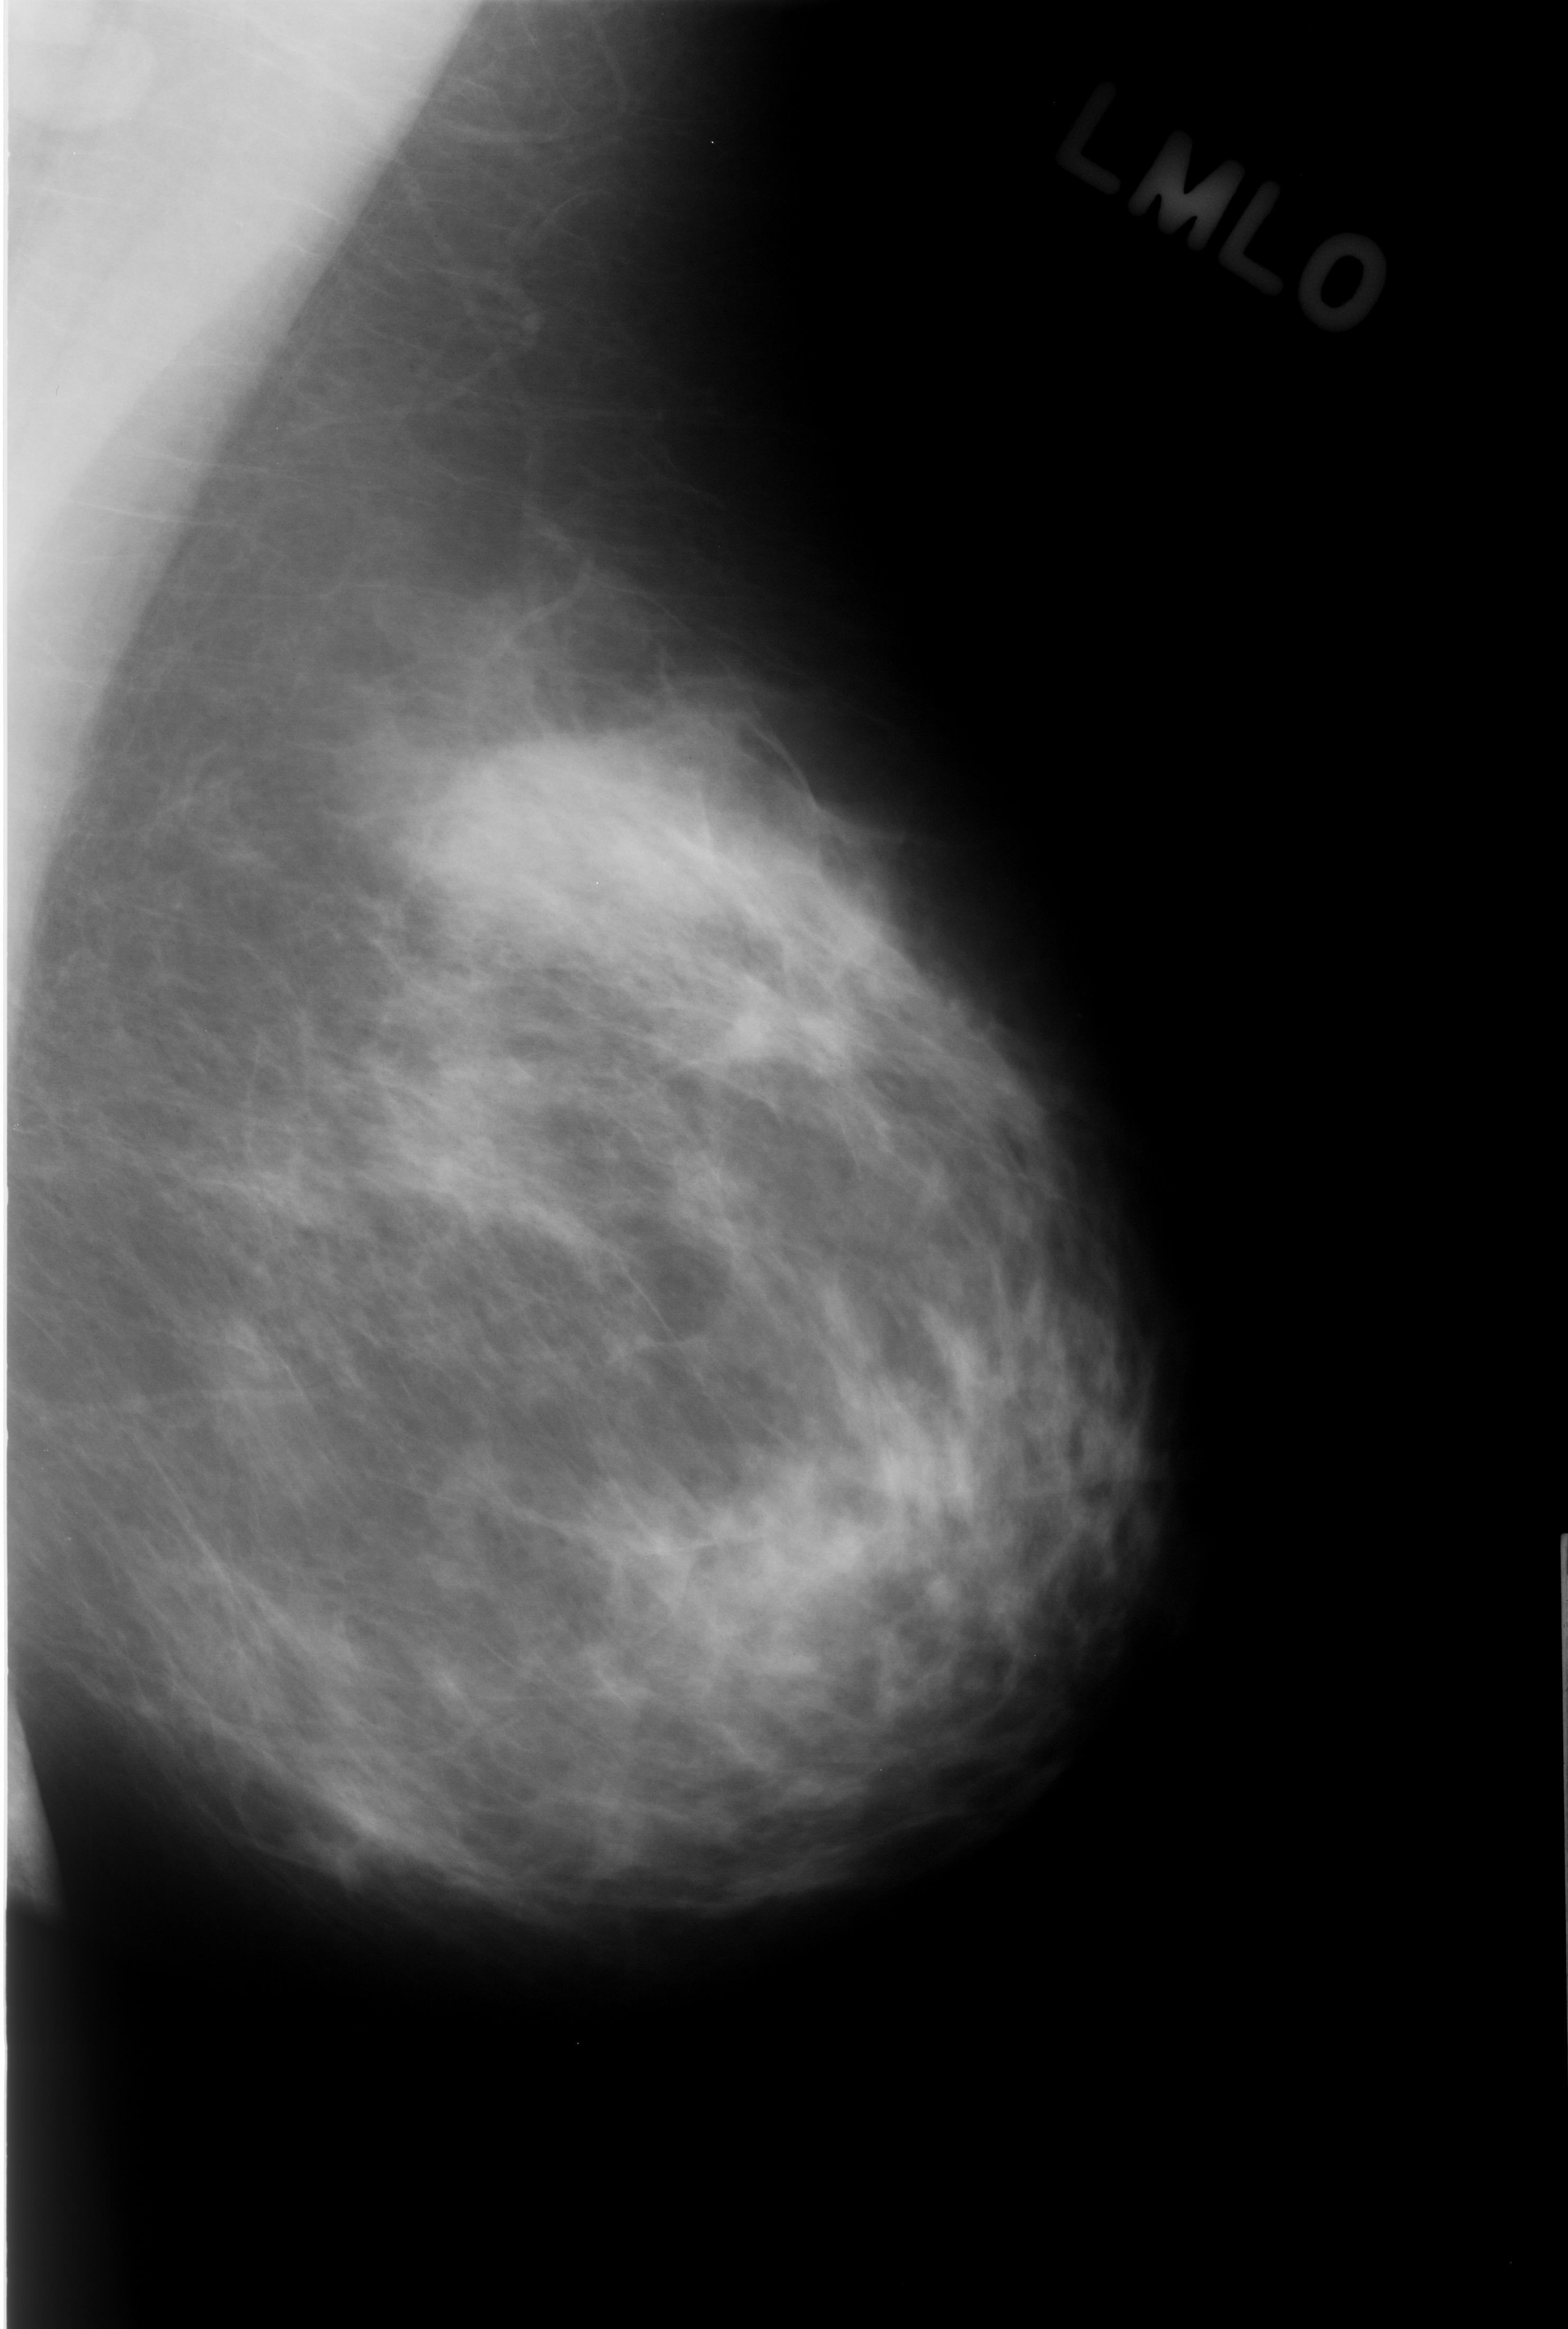
Digitized screen-film mammogram; left breast; MLO view.
Finding: mass, shape asymmetric breast tissue; BI-RADS assessment category 3; benign without callback (not worked up further).